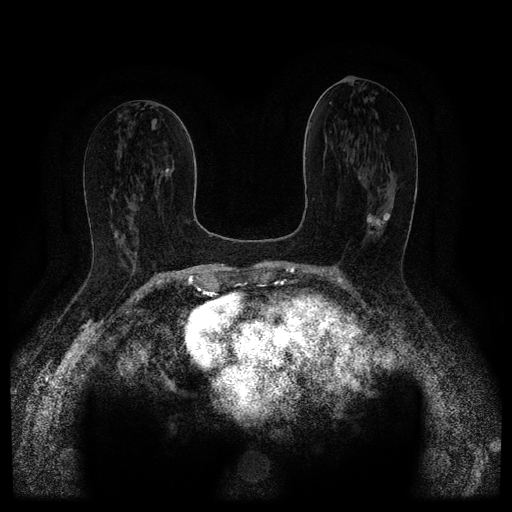
Breast MRI (dynamic contrast-enhanced, multi-phase), one axial slice. Position 53 of 116 along the scan axis. Dynamic contrast-enhanced series, time point 2 of 5 at this slice position (early post-contrast). 1.5 T. TE 2.6 ms, TR 5.4 ms. 512 × 512 image matrix. Patient: female, 67 years.
Outlined on this slice (semi-automatically segmented with operator editing):
- breast lesion (labelled 'tumour' in the annotation; benign lesions carry a separate 'benign' label): bounding box [x1, y1, x2, y2] px = [366, 213, 390, 234]